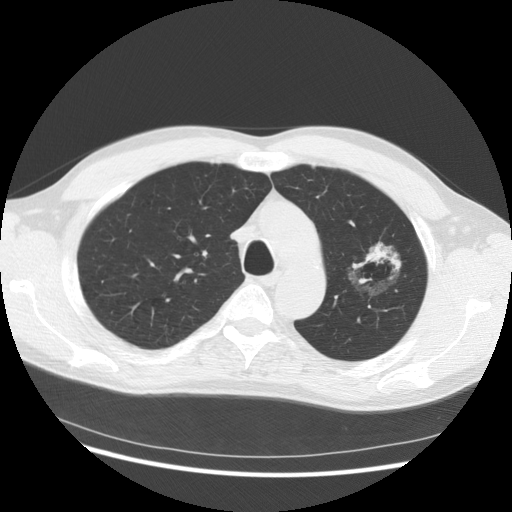
Chest CT (low-dose screening protocol), one axial image; third annual screen; lung window (W 1500 / L -600 HU); 2.5 mm slice thickness; standard (soft-tissue) reconstruction kernel (STANDARD); slice 105 of 145 in the series; 512 × 512 image matrix. Male participant, aged 61 years at enrolment.
- Lesion marked by an expert reader, bounding box <332,231,410,311> (left, top, right, bottom; pixels).
- Screening reader's record for this exam (one nodule recorded; not confirmed to be the boxed lesion): non-calcified nodule or mass ≥4 mm, left upper lobe, 37 × 33 mm, poorly defined margins, mixed attenuation, pre-existing on the prior screen: yes; interval growth: yes.
- Lung cancer was diagnosed 361 days after this screen: bronchiolo-alveolar adenocarcinoma, NOS, left upper lobe, well differentiated (G1), stage IB (AJCC 6th edition), 44 mm at pathology.